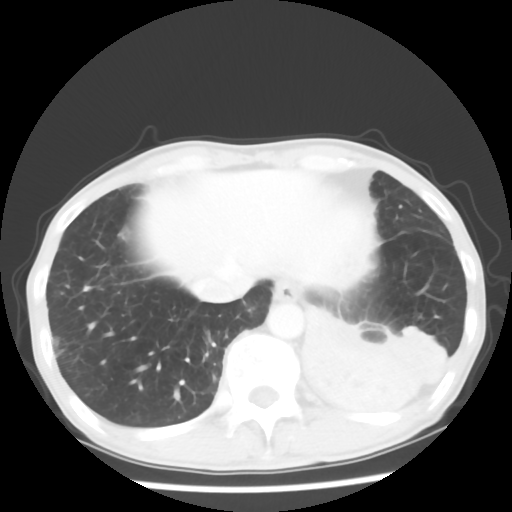
Chest CT, one axial slice; slice 11 of 64 in the series (ordered by position); lung window (W 1500 / L -600 HU); 5 mm slice thickness; 512 × 512 image matrix, field of view 313 × 313 mm. Male patient, age 68 years. Case-level facts recorded for this patient, not image findings: clinical TNM (as recorded): T4 N0 M0.
Annotated regions visible in this slice (rectangle marked by the reading radiologist):
- lung tumour (recorded histology: squamous cell carcinoma): bounding box [x1, y1, x2, y2] px = [285, 301, 448, 423]